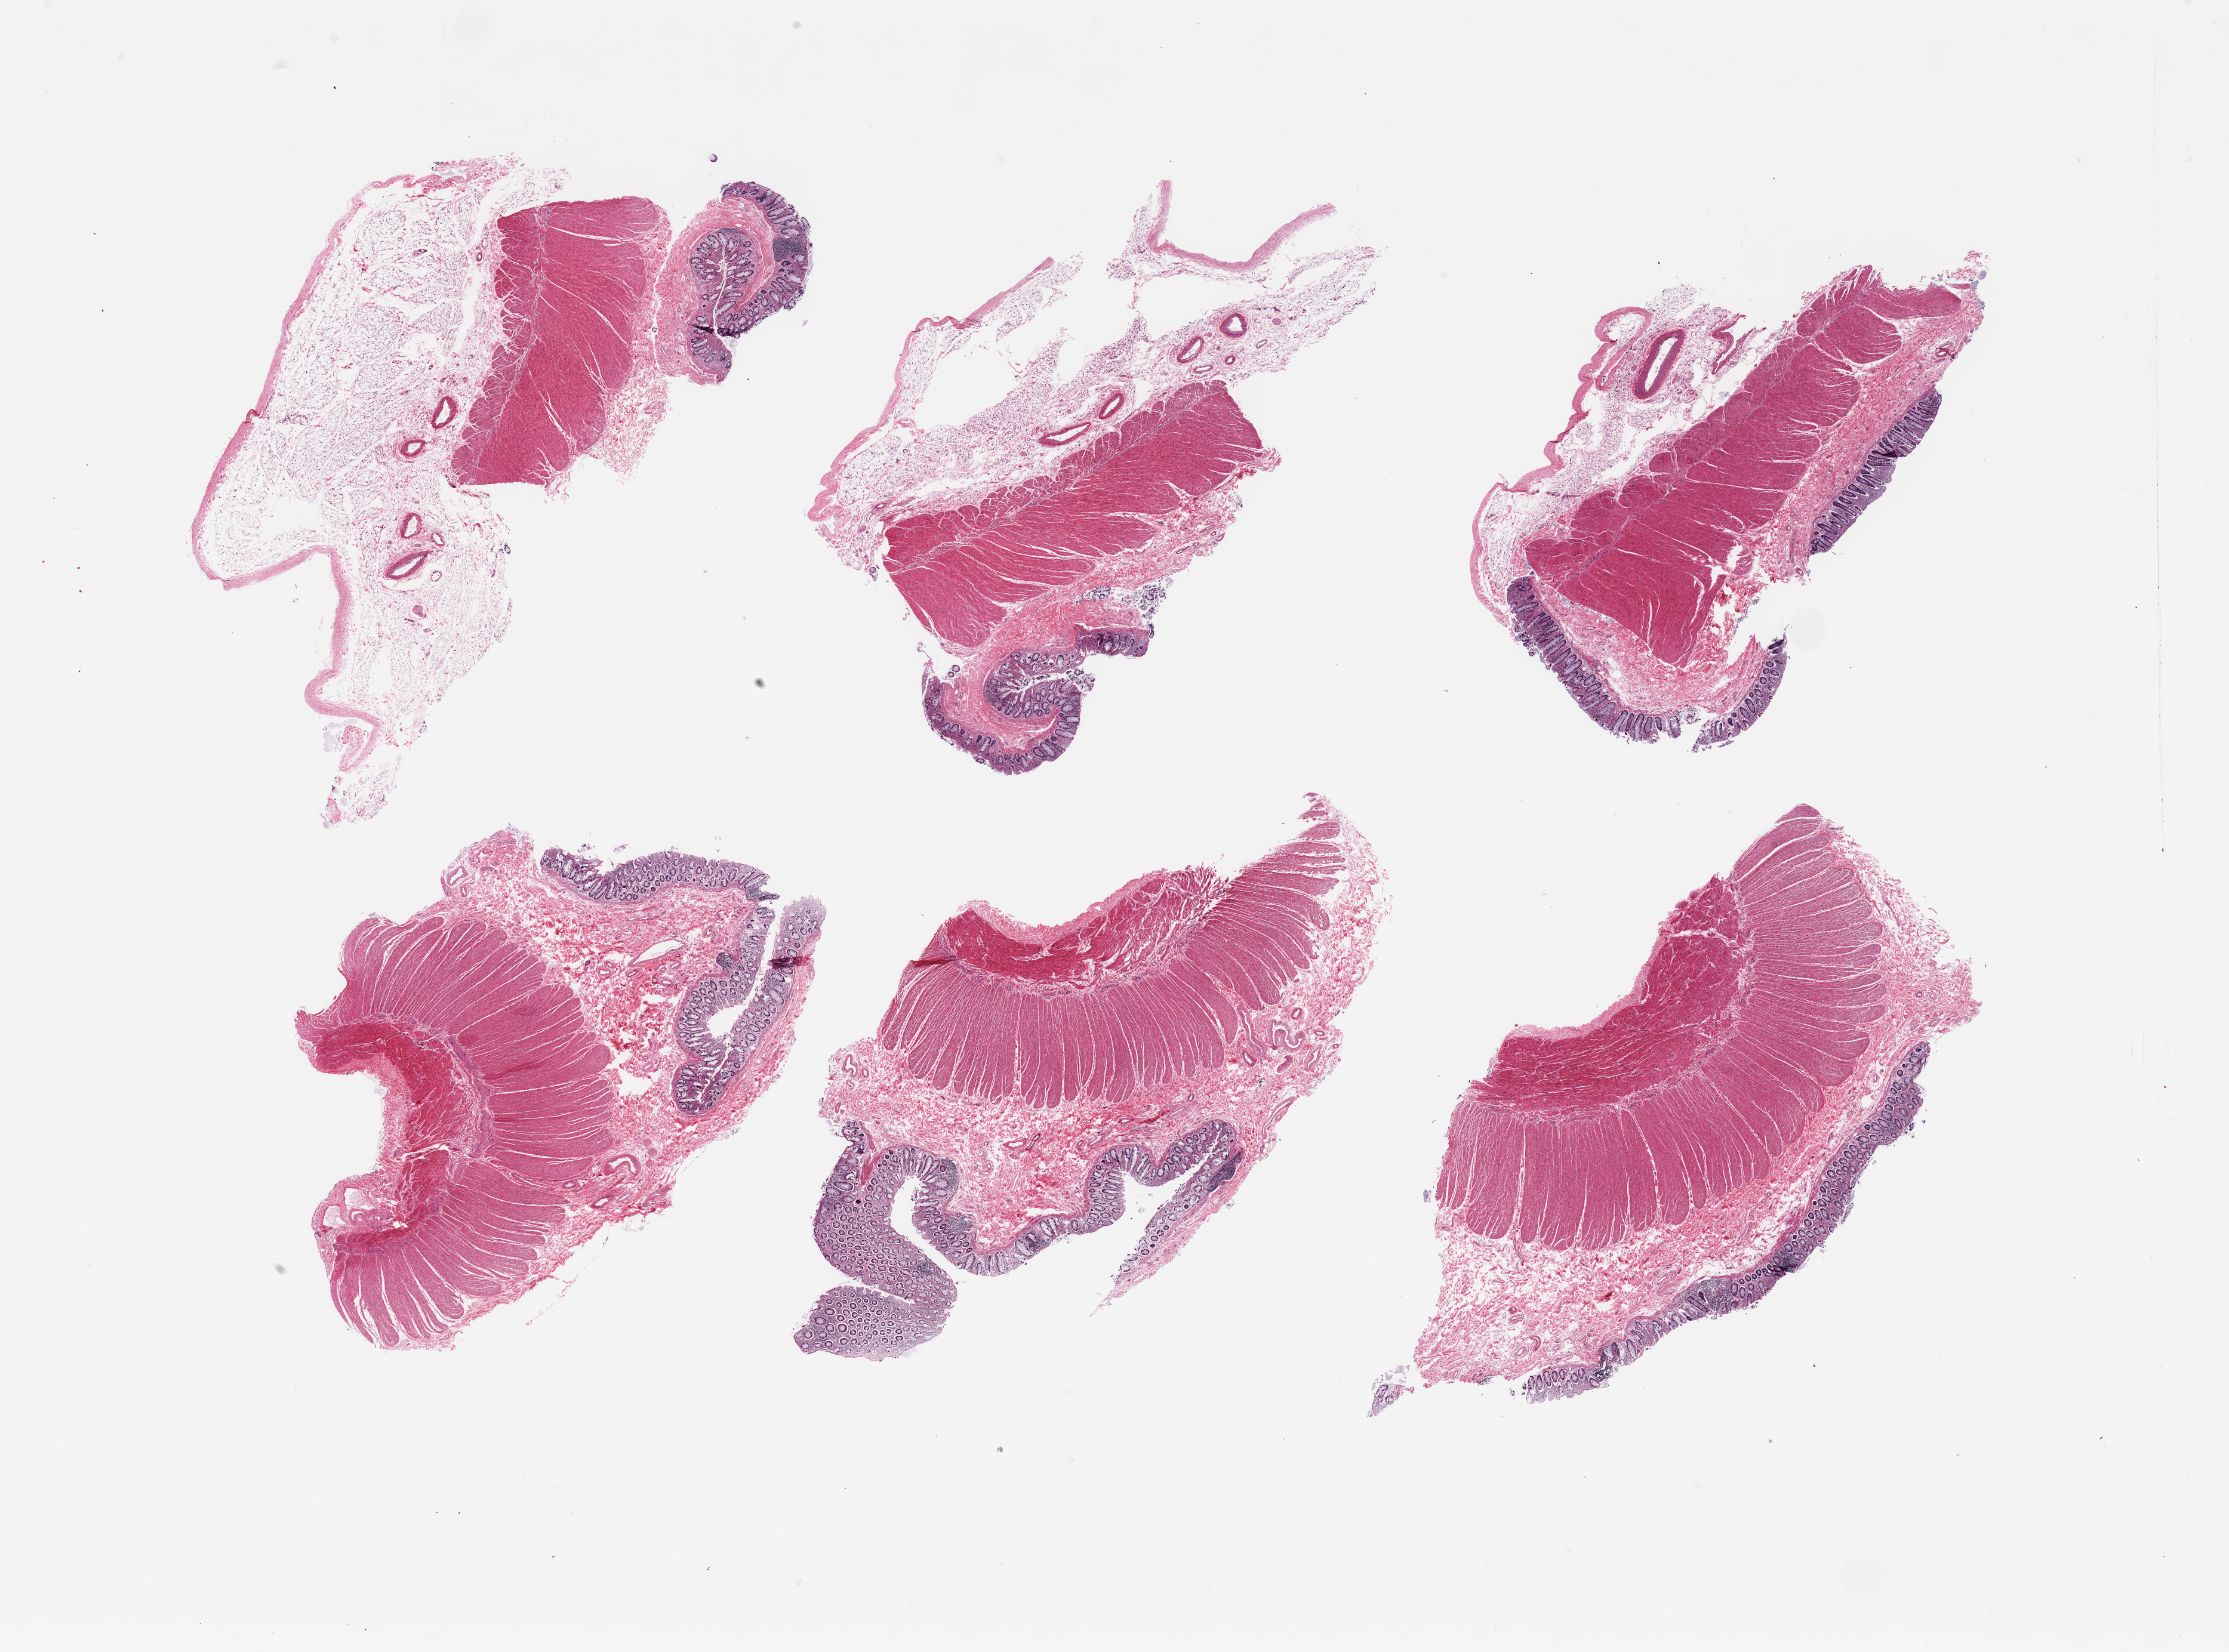
Whole-slide image, hematoxylin and eosin (H&E) stain, brightfield, shown as a low-resolution overview of the whole scanned area (about 29.5 x 21.9 mm). PAXgene-fixed paraffin-embedded (PFPE) section. Sampled site (target tissue): sigmoid colon. Donor tissue sample. Male donor.
Review note (as recorded): 6 pieces; moderately autolyzed non target mucosa; well preserved target muscularis; attached serosa and fat.